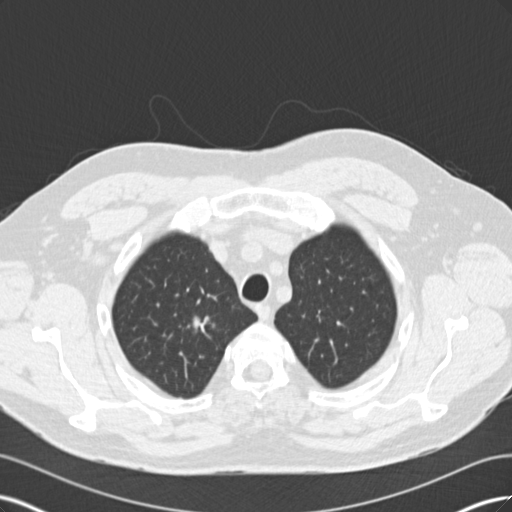
Low-dose screening chest CT, one axial slice; position 146 of 171 along the scan axis; reconstruction kernel B30f; 120 kVp; lung window (W 1500 / L -600 HU); 512 × 512 image matrix, field of view 360 × 360 mm.
Outlined on this slice (expert manual segmentation):
- lesion 1 (tumor, upper lobe of right lung): box from (x=187, y=316) to (x=215, y=337) px